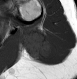
MRI of an extremity soft-tissue mass, one axial slice; slice 14 of 28 in the series (ordered by position); MR volume resampled by the dataset authors to the PET/CT grid (not the native acquisition matrix); 3.27 mm slice thickness; 77 × 79 image matrix, field of view 75 × 77 mm. Female patient. From the clinical record (not read from this slice): histological type: malignant fibrous histiocytoma; grade: low; site of the primary tumour: left arm.
Annotated regions visible in this slice (expert contour drawn on MRI and transferred to this co-registered scan by the dataset authors):
- gross tumour volume (mass): box from (x=21, y=29) to (x=57, y=62) px